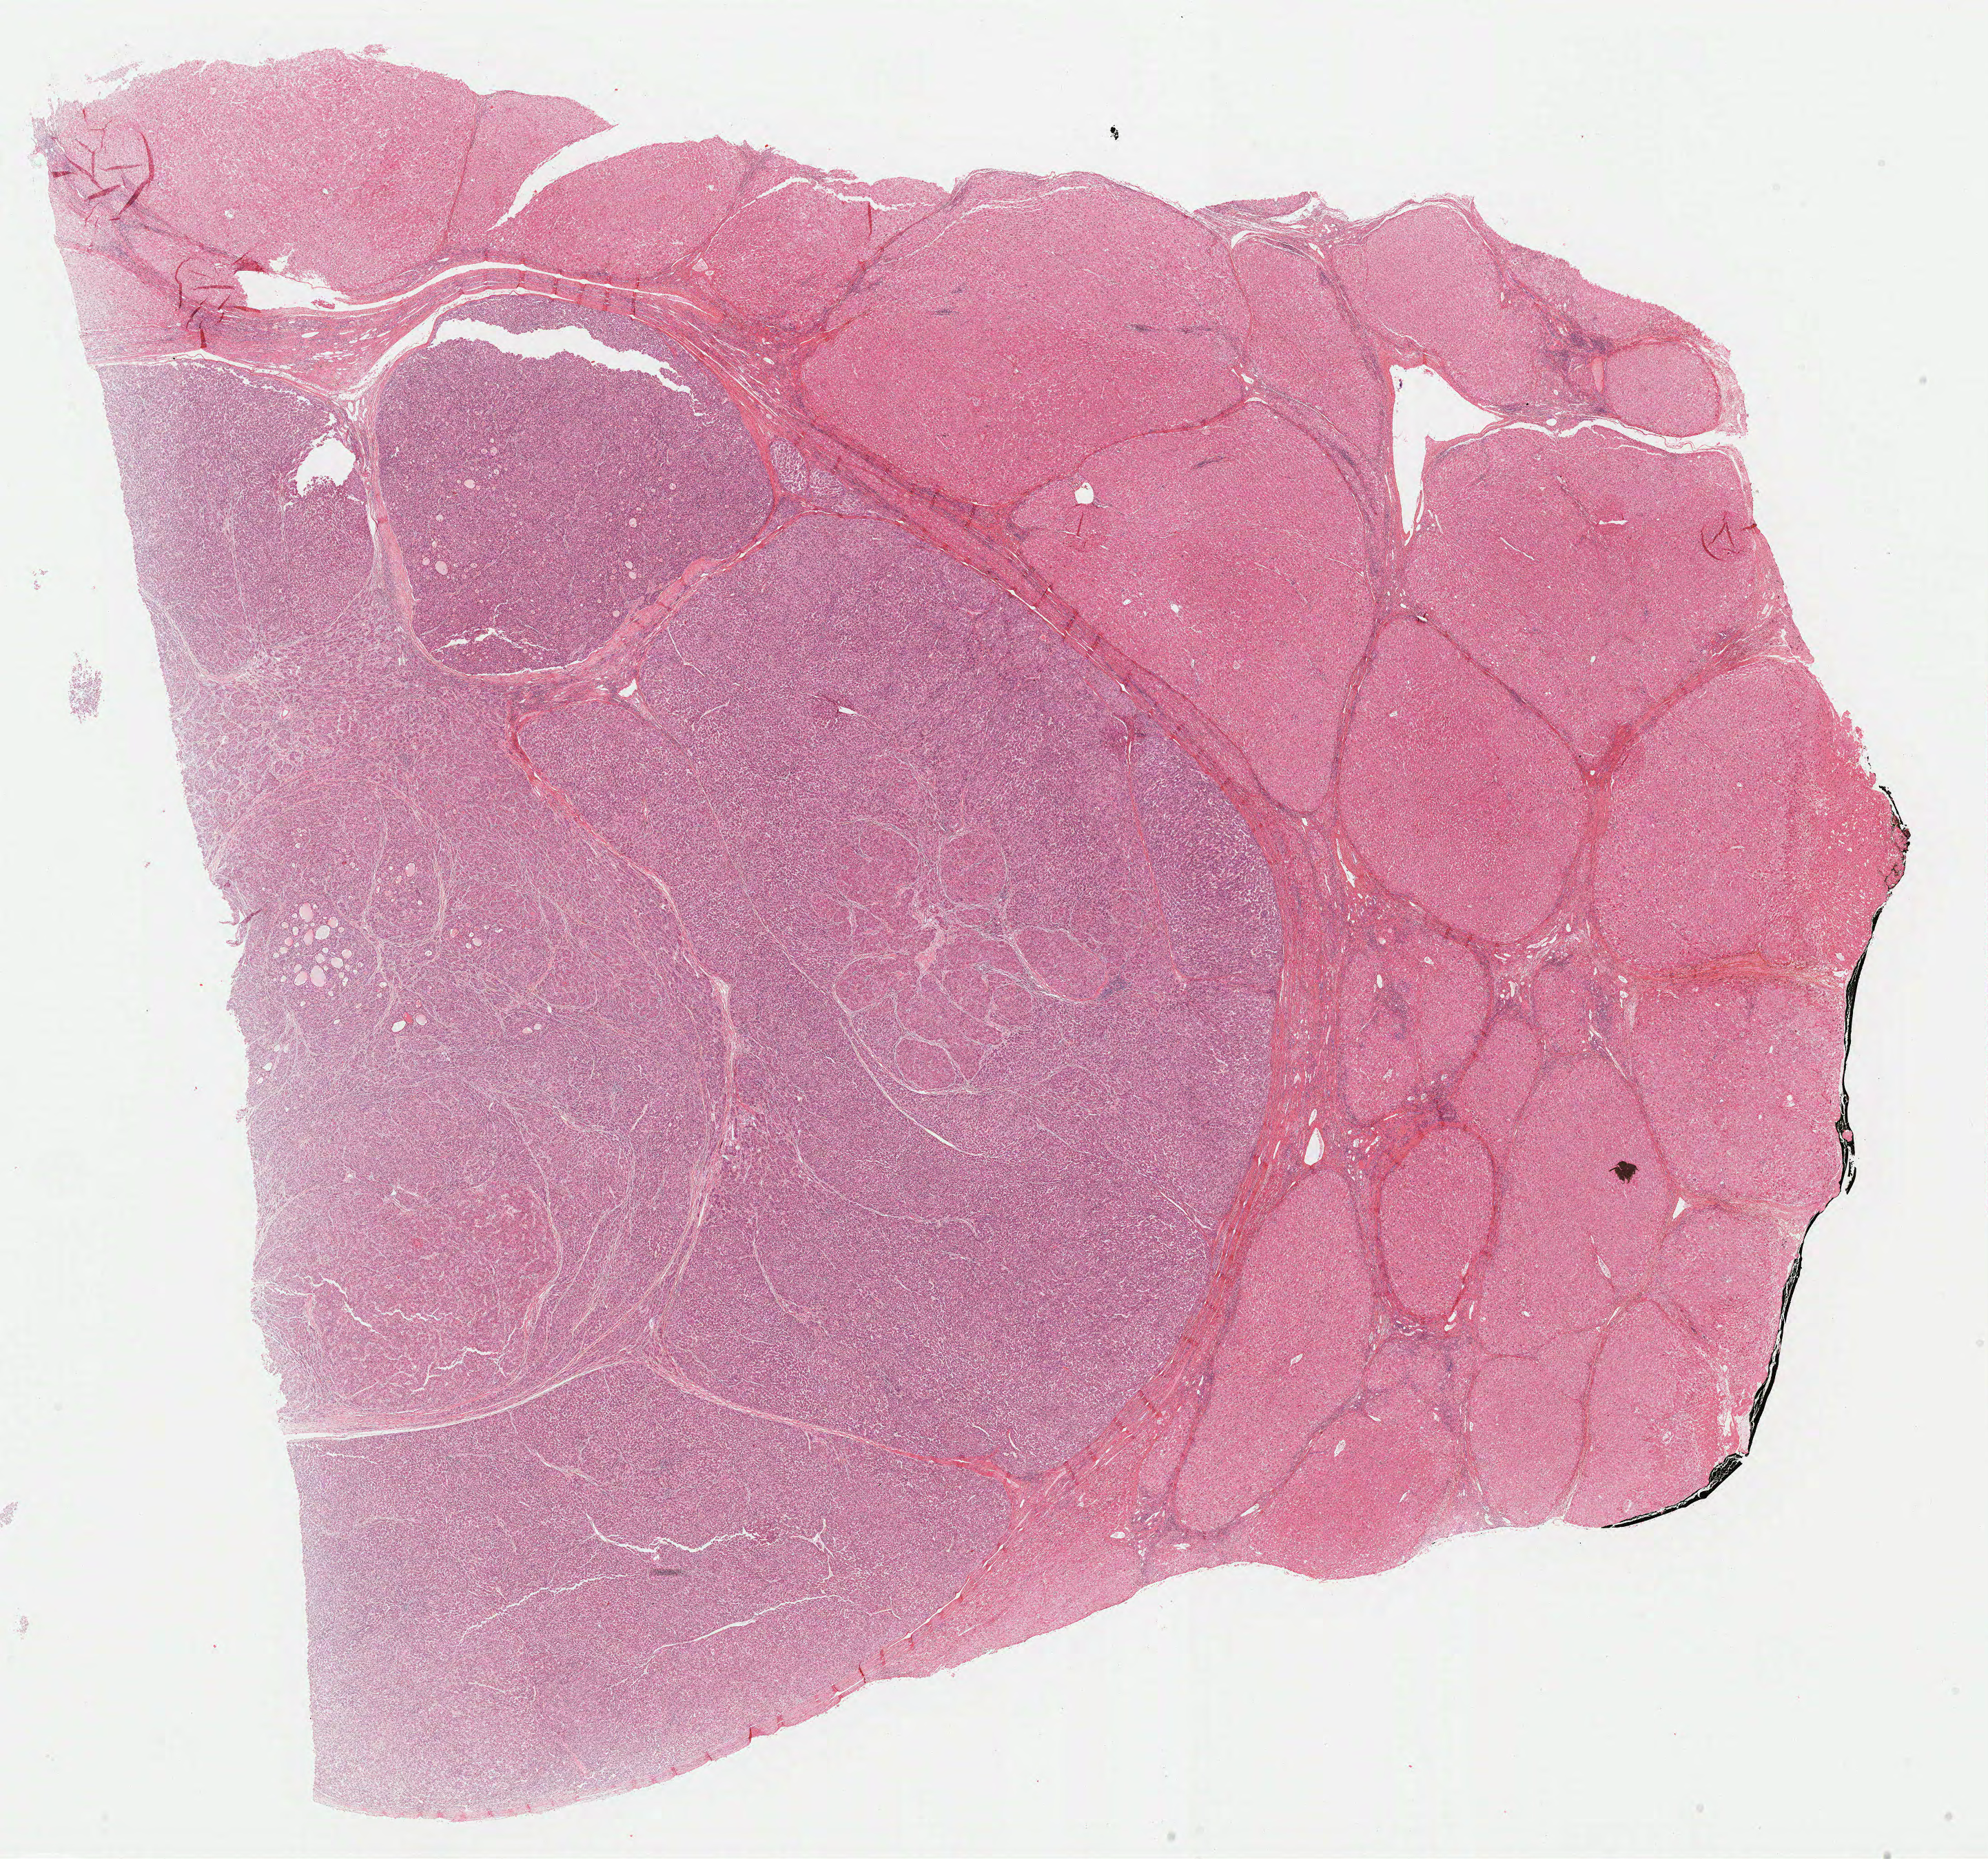
Whole-slide histology image, Hematoxylin and eosin (H&E) stained, whole scanned area (about 22.8 x 21.3 mm, slide scanned at 40x) shown as a low-resolution overview; FFPE section; primary tumour sample from the liver. Patient: male, age at initial diagnosis 38 years. Histologic grade: G2 (moderately differentiated).
AJCC pathologic stage: I (6th edition). TNM: T1 N0 M0. Diagnosis: Hepatocellular carcinoma, NOS.